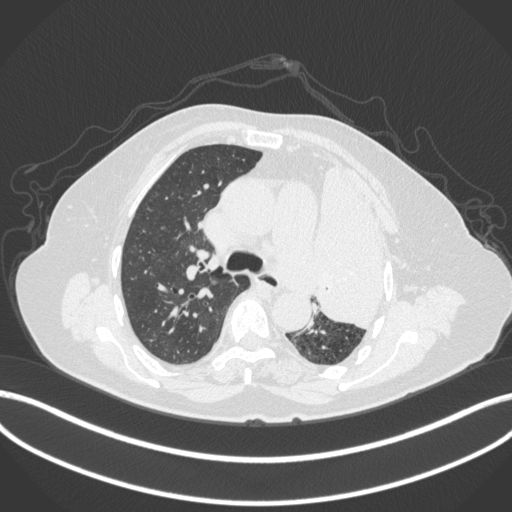
Chest CT, one axial slice. Position 258 of 399 along the scan axis. Reconstruction kernel B31f. 120 kVp. Lung window (W 1500 / L -600 HU). 512 × 512 image matrix. Patient: female, 75 years. From the clinical record (not read from this slice): clinical TNM (as recorded): T3 N3 M1.
Outlined on this slice (rectangle marked by the reading radiologist):
- lung tumour (recorded histology: adenocarcinoma): bounding box <308,157,402,336> (left, top, right, bottom; pixels)